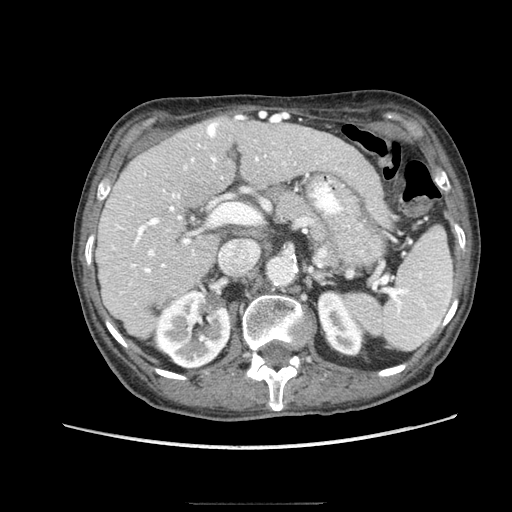
Contrast-enhanced abdominal CT (liver protocol), one axial slice; position 47 of 83 along the scan axis; soft-tissue window (W 400 / L 40 HU); 512 × 512 image matrix. Case-level facts recorded for this patient, not image findings: diagnosis: hepatocellular carcinoma (patient treated with transarterial chemoembolisation; whether this scan precedes or follows treatment is not stated here); TNM stage (as recorded): Stage-I; Child-Pugh class: A; tumour differentiation: moderately differentiated; tumour nodularity: uninodular.
Annotated regions visible in this slice (semi-automatically segmented with operator editing):
- liver parenchyma outside the tumour (the mass and vessels are separate outlines, so this box may not span the whole liver): box from (x=96, y=114) to (x=372, y=338) px
- liver vessels: (x=103, y=115)–(x=337, y=294)